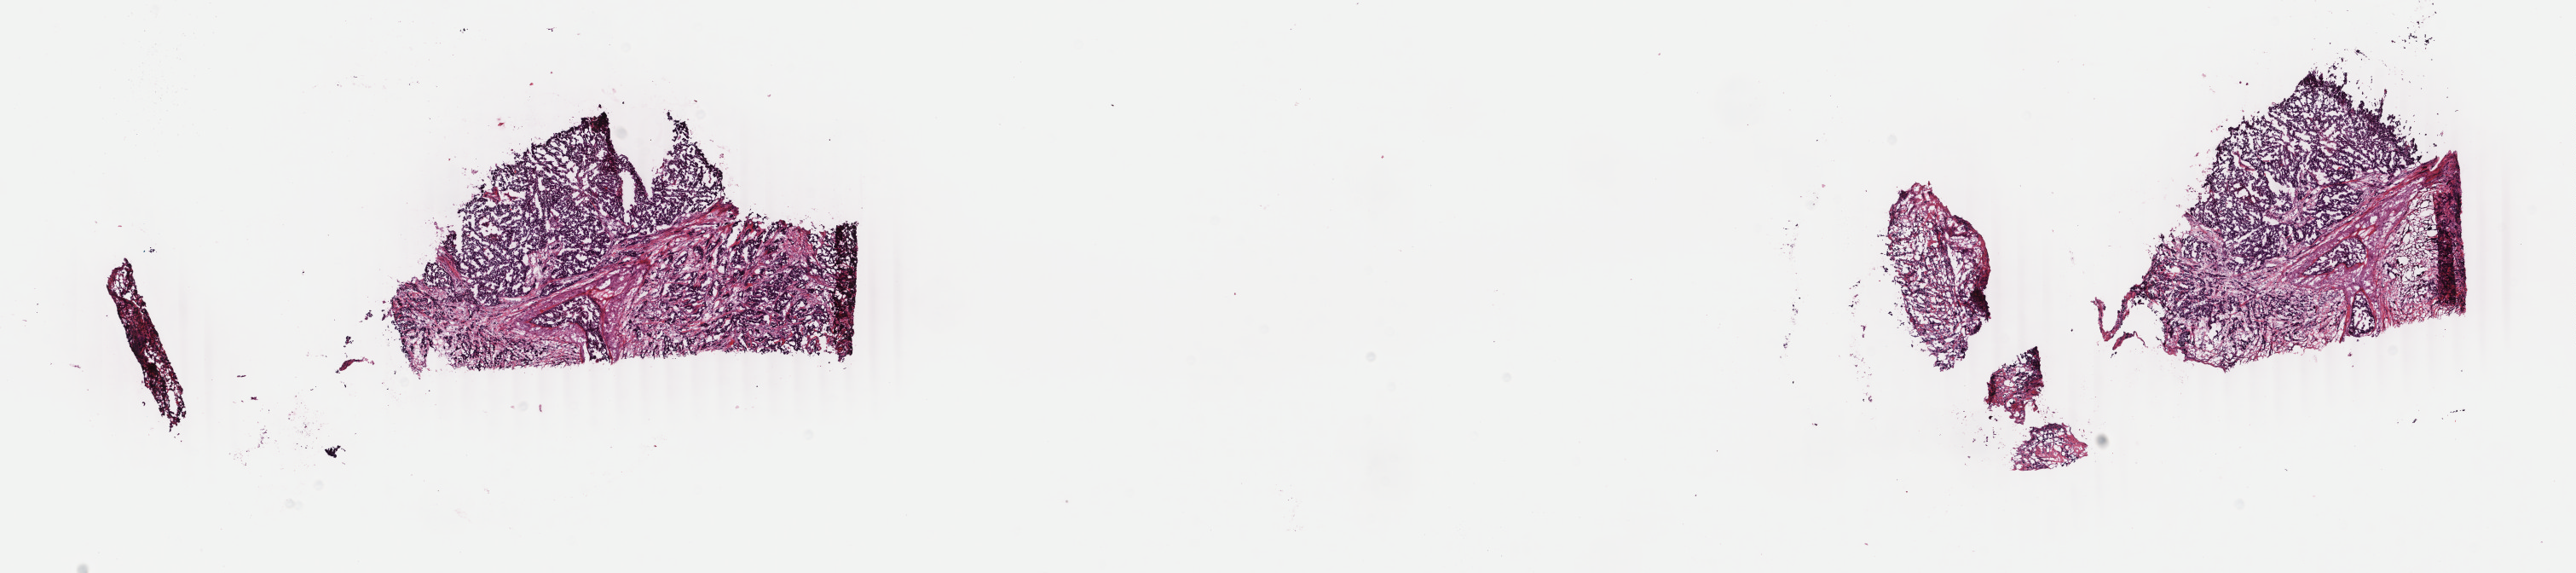
Whole-slide histology image, H&E — shown as a low-resolution overview of the whole scanned area (about 24.0 x 5.3 mm, from a 40x scan); frozen section from the top of the tissue portion; sample: primary tumour, breast. Patient: female, age at initial diagnosis 60 years. Slide review estimates, as recorded: tumour cells 80%, tumour nuclei 80%, normal cells 0%, stromal cells 19%, necrosis 1%. Infiltration values recorded for this section: lymphocyte infiltration 2%, monocyte infiltration 0%, neutrophil infiltration 0%.
- pathologic diagnosis: Infiltrating duct carcinoma, NOS
- AJCC pathologic stage: IIA
- lymph nodes positive (case pathology): 0 of 16 examined